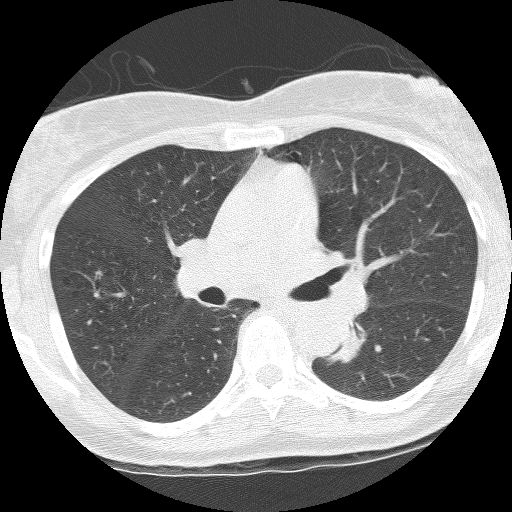
Chest CT (low-dose screening protocol), one axial image, third annual screen, lung window (W 1500 / L -600 HU), 2.5 mm slice thickness, slice 52 of 115 in the series. Female participant, aged 62 years at enrolment. Former smoker at enrolment.
Expert reader's lesion annotation, bounding box (x1, y1, x2, y2) in pixels: (324, 319, 382, 362). The screening reader recorded 3 non-calcified nodules or masses ≥4 mm on this exam (right upper lobe, left lower lobe, left upper lobe); which of them this box marks is not recorded. Later outcome: lung cancer diagnosed 165 days after this screen — squamous cell carcinoma, NOS, left lower lobe, stage IIIB (AJCC 6th edition), 31 mm at pathology.